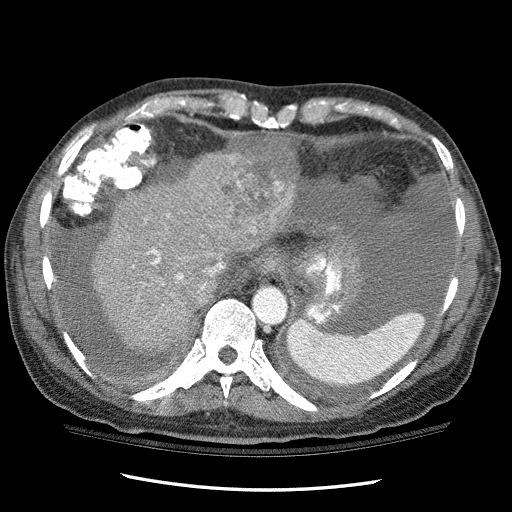
Contrast-enhanced abdominal CT (liver protocol), one axial slice. Position 89 of 114 along the scan axis. Reconstruction kernel STANDARD. One of 3 acquisitions stored at this slice position. Soft-tissue window (W 400 / L 40 HU). 512 × 512 image matrix, field of view 360 × 360 mm. Case-level facts recorded for this patient, not image findings: diagnosis: hepatocellular carcinoma (patient treated with transarterial chemoembolisation; whether this scan precedes or follows treatment is not stated here); TNM stage (as recorded): Stage-I; Child-Pugh class: C; tumour differentiation: well differentiated; tumour nodularity: uninodular.
Structures marked on this image (semi-automatically segmented with operator editing):
- liver parenchyma outside the tumour (the mass and vessels are separate outlines, so this box may not span the whole liver): bounding box (x1, y1, x2, y2) in pixels: (91, 152, 278, 356)
- mass: (186, 134, 299, 239)
- liver vessels: (132, 214, 224, 289)